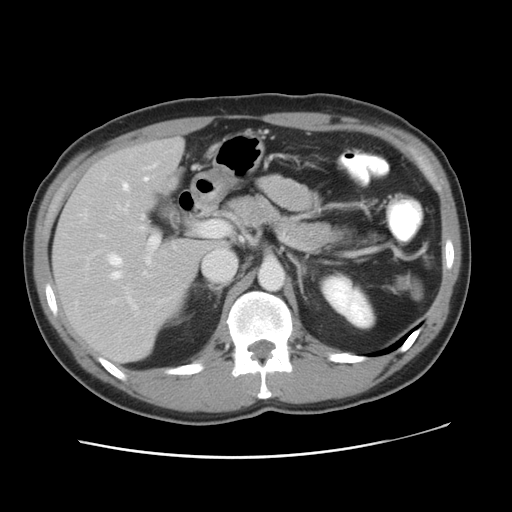
Contrast-enhanced abdominal CT, one axial slice; slice 29 of 49 in the series (ordered by position); 120 kVp; intravenous contrast given; soft-tissue window (W 400 / L 40 HU); 5 mm slice thickness; 512 × 512 image matrix. Male patient, age 41 years. From the clinical record (not read from this slice): diagnosis: colorectal cancer liver metastases, imaged before liver resection; multiple liver metastases: yes; largest metastasis: 0.7 cm.
Annotated regions visible in this slice (manually delineated by an expert):
- hepatic veins: bounding box (x1, y1, x2, y2) in pixels: (107, 163, 238, 280)
- liver: (54, 140, 218, 363)
- planned liver remnant (the part of the liver to remain after resection): (105, 140, 183, 200)
- portal vein (with intrahepatic branches): (129, 221, 212, 307)
- liver metastasis: (153, 323, 159, 328)
- liver metastasis: (152, 322, 158, 328)